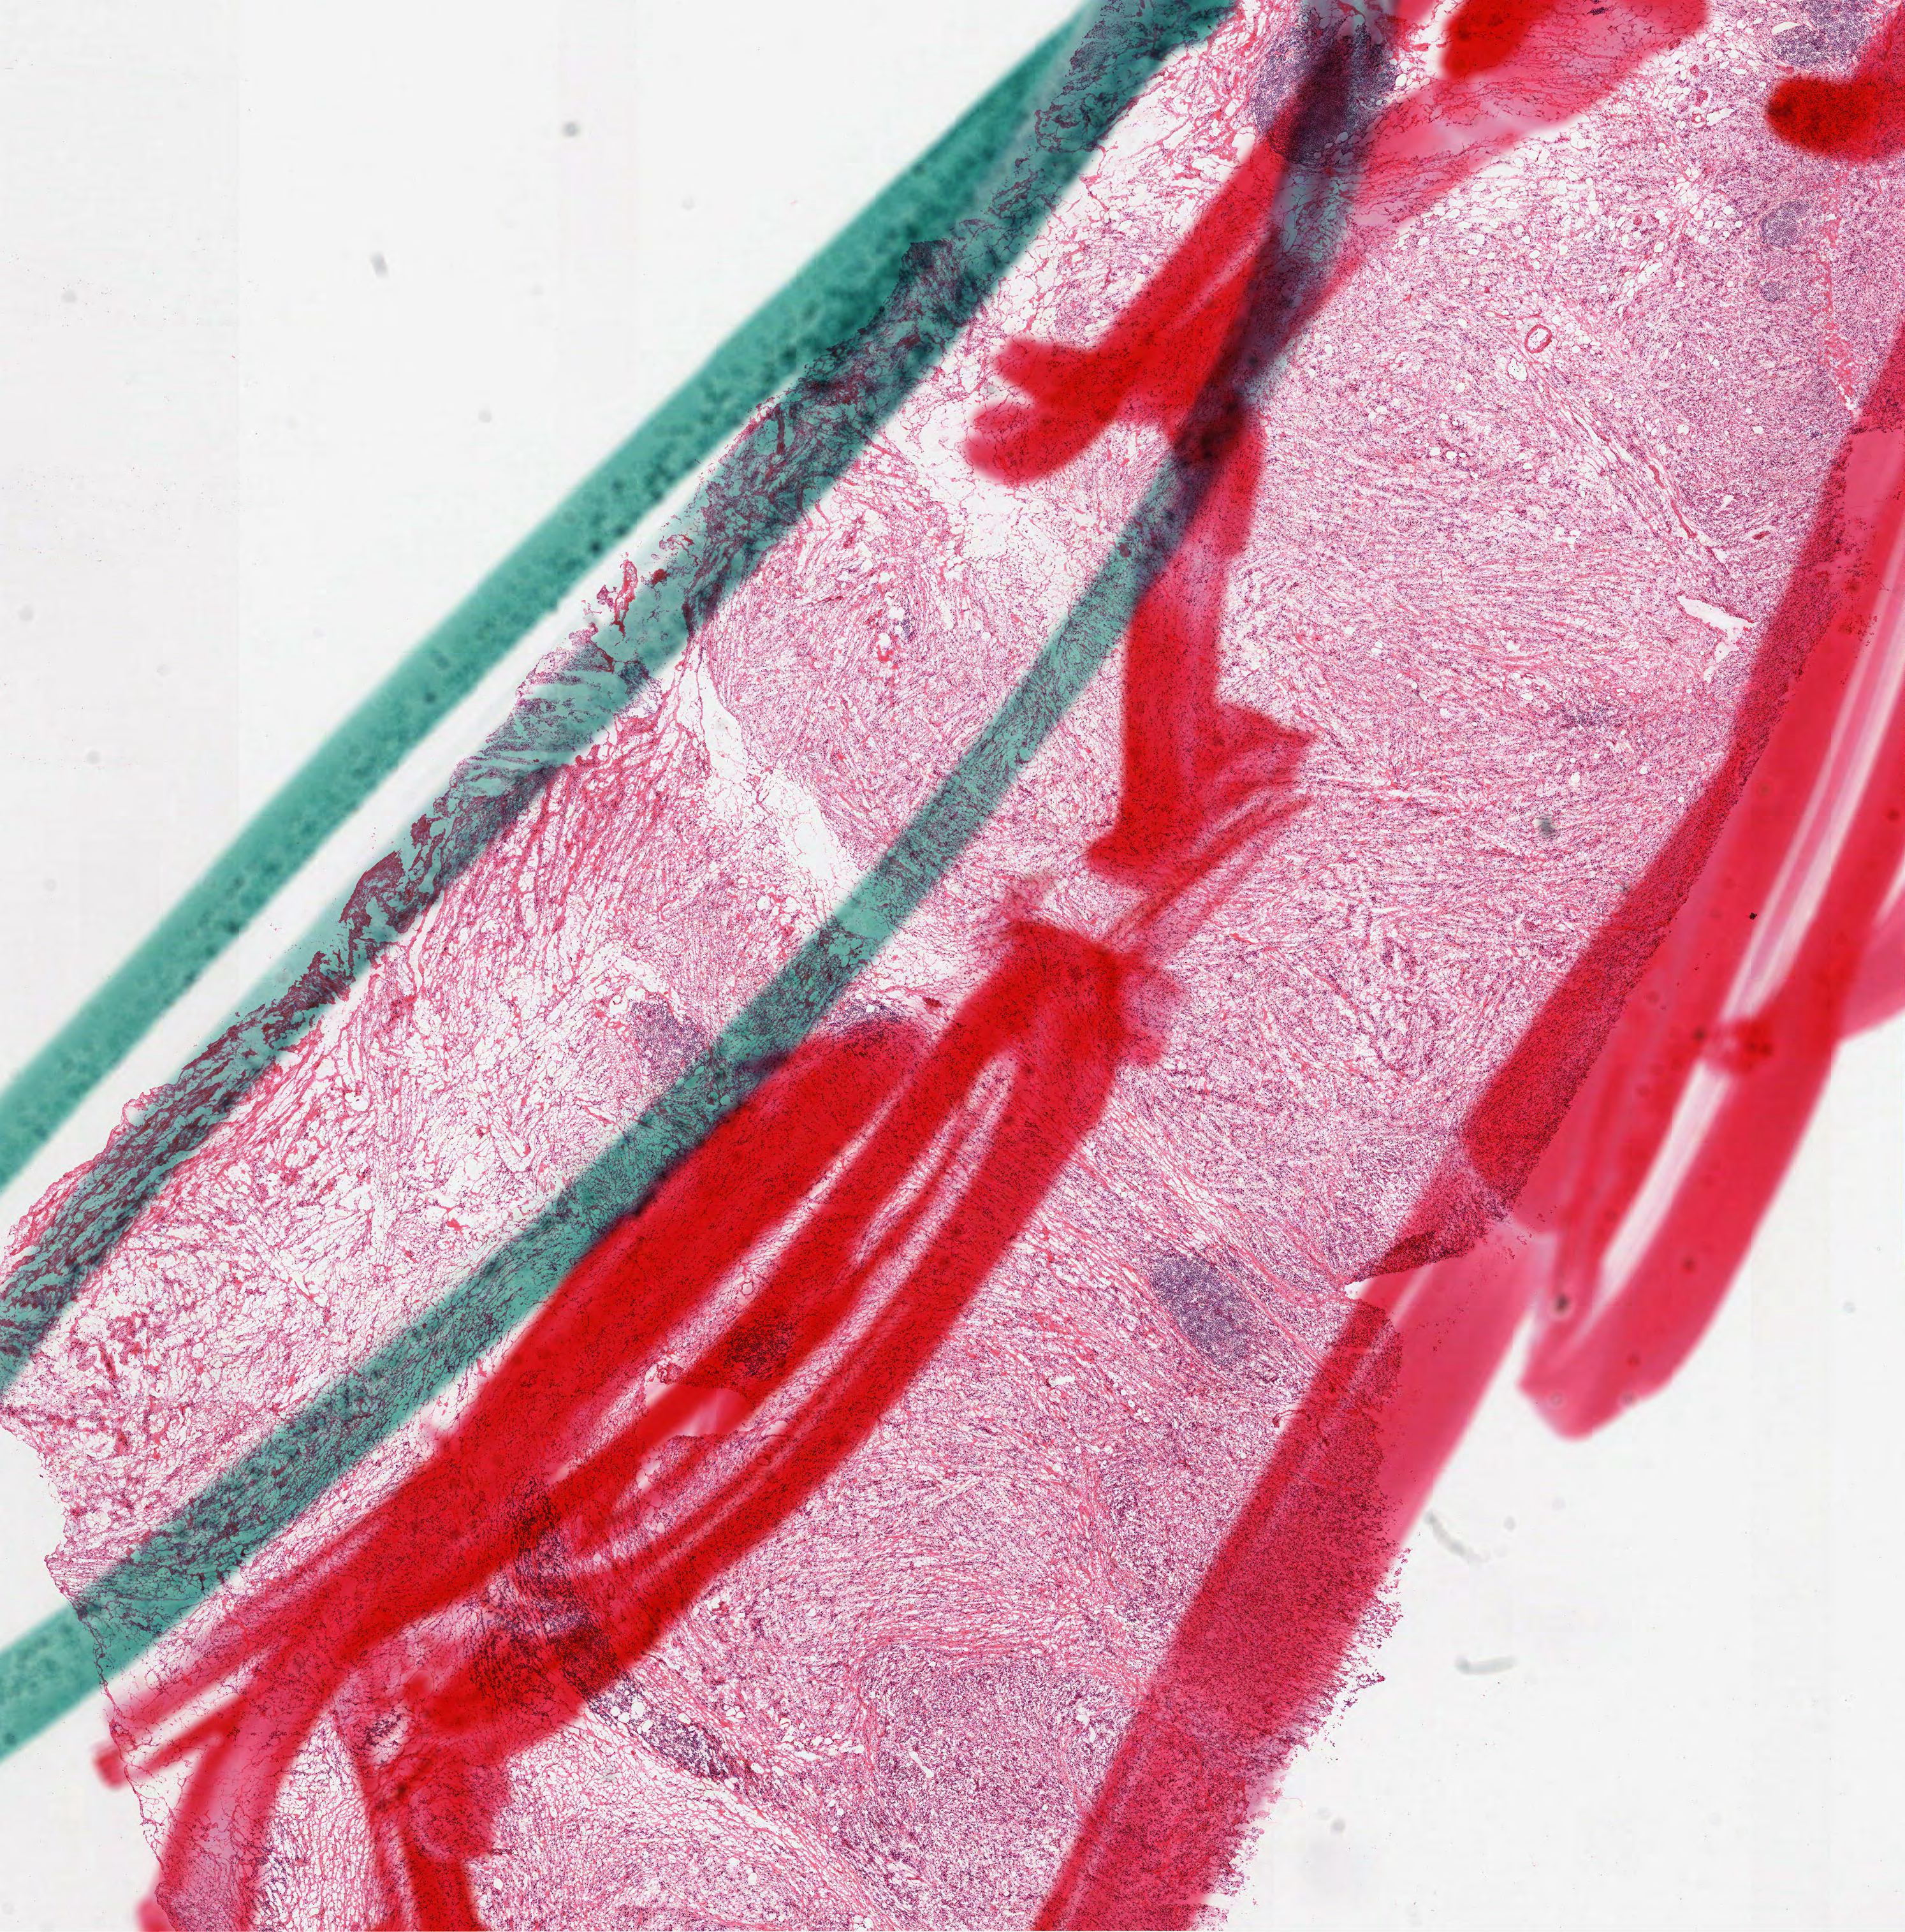
Whole-slide histology image, H&E, low-resolution overview of the scanned area, about 12.0 x 12.2 mm (from a 40x scan). Frozen section from the top of the tissue portion. Sample: primary tumour, stomach. Male, age 54 years at initial diagnosis. Histologic grade: G3 (poorly differentiated). Slide review estimates, as recorded: tumour cells 70%, tumour nuclei 70%, normal cells 30%, stromal cells 0%, necrosis 0%. Infiltration values recorded for this section: lymphocyte infiltration 10%, monocyte infiltration 0%, neutrophil infiltration 10%.
* histologic diagnosis: Adenocarcinoma, NOS
* lymph nodes positive (case pathology): 1 of 2 examined
* AJCC pathologic stage: IIA (7th edition)